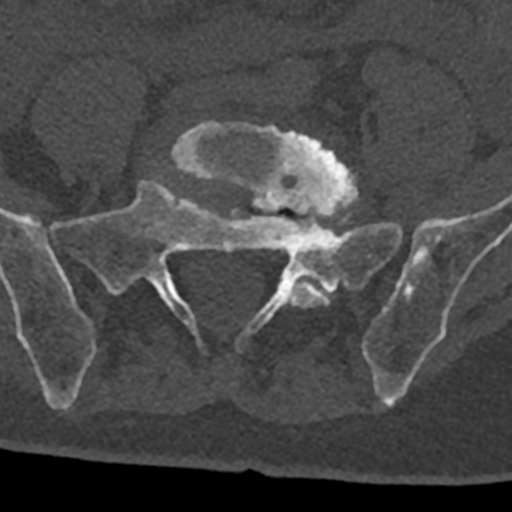
CT including the spine, one axial slice. Position 167 of 797 along the scan axis. Reconstruction kernel Br40s/3. Bone window (W 1800 / L 400 HU). 0.5 mm slice thickness. 512 × 512 image matrix, field of view 160 × 160 mm. Male patient, age 74 years. Case-level facts recorded for this patient, not image findings: primary cancer: renal.
Annotated regions visible in this slice (semi-automatically segmented with operator editing):
- L5 vertebra: bounding box <170,122,358,308> (left, top, right, bottom; pixels)